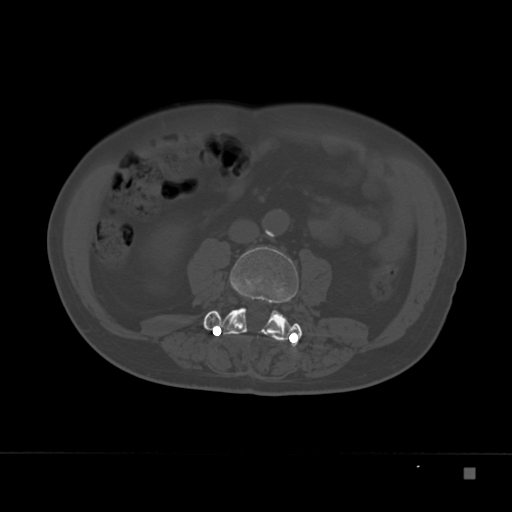
CT including the spine, one axial slice. Position 60 of 332 along the scan axis. Bone window (W 1800 / L 400 HU). 512 × 512 image matrix, field of view 389 × 389 mm. Male patient, age 72 years. From the clinical record (not read from this slice): primary cancer: skeletal.
Outlined on this slice (semi-automatically segmented with operator editing):
- L3 vertebra: bounding box <204,246,302,341> (left, top, right, bottom; pixels)
- L4 vertebra: <204,311,299,345>